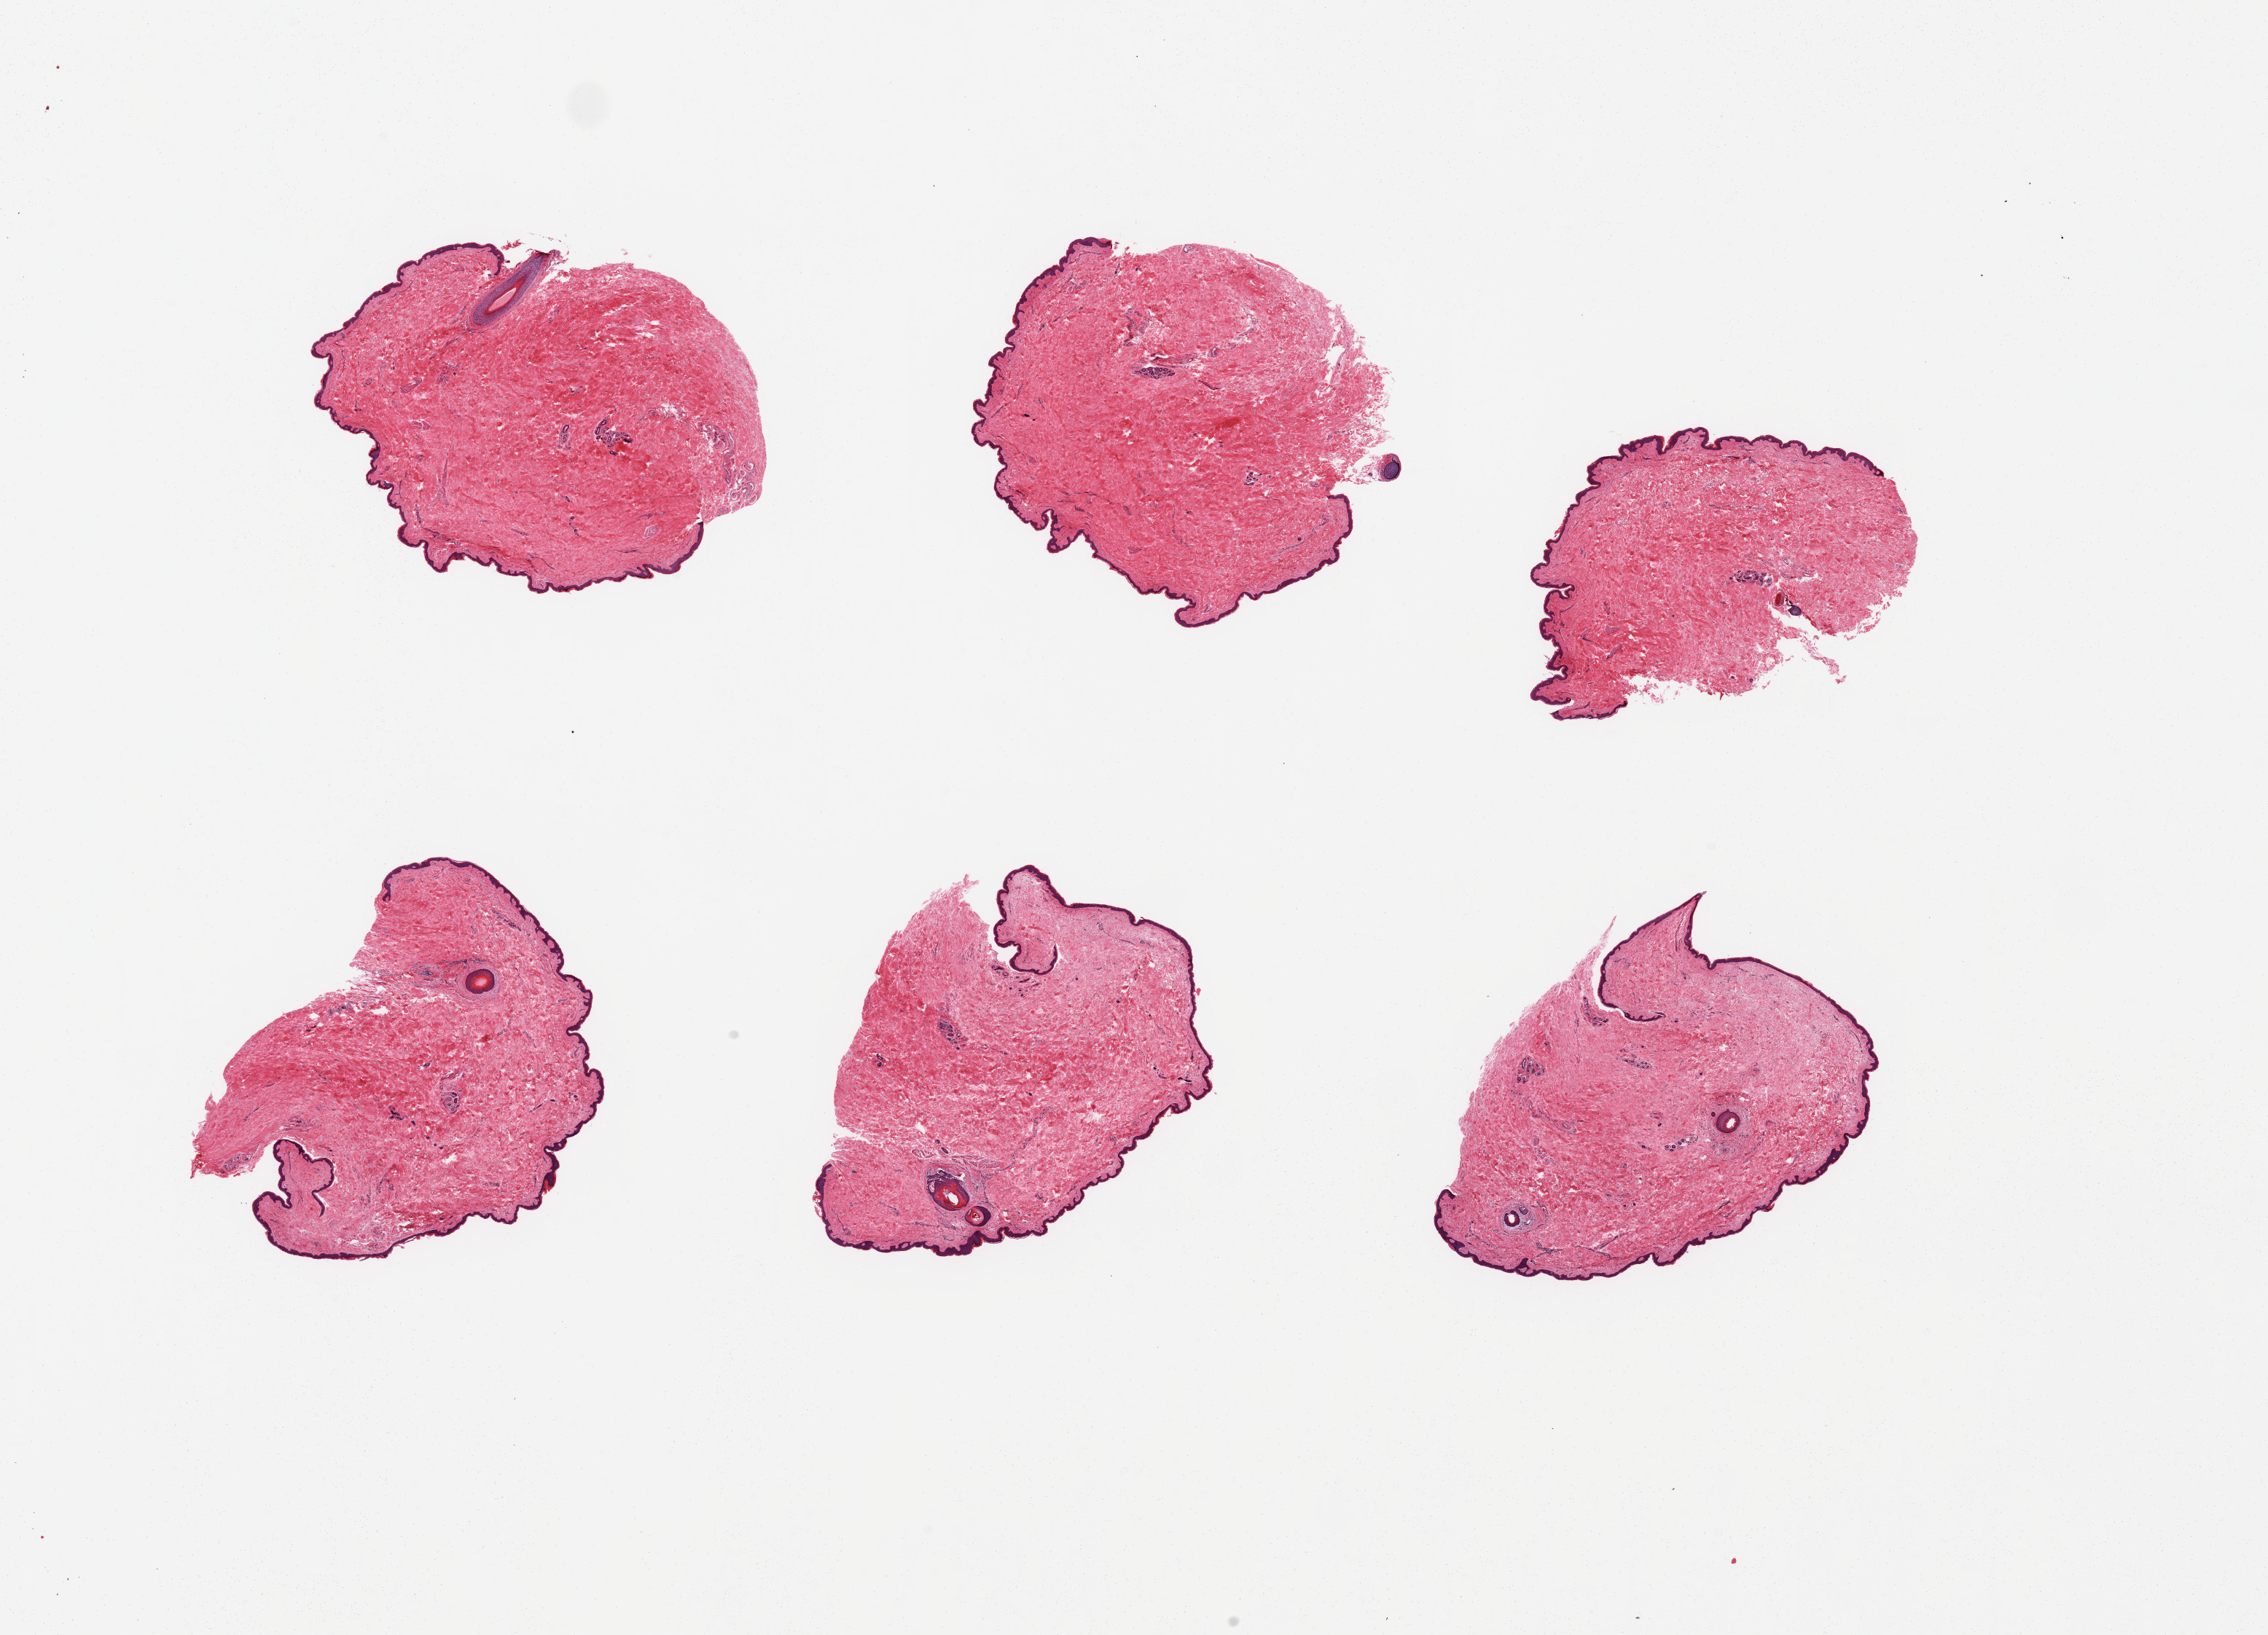
Haematoxylin and eosin whole-slide image — shown as a low-resolution overview of the whole scanned area (about 24.6 x 17.7 mm), PAXgene-fixed paraffin-embedded (PFPE) section, target tissue: skin of suprapubic region, donor tissue sample. Donor sex: male.
- review note (as recorded): 6 pieces, no dermal fat; squamous epithelium is ~30 microns